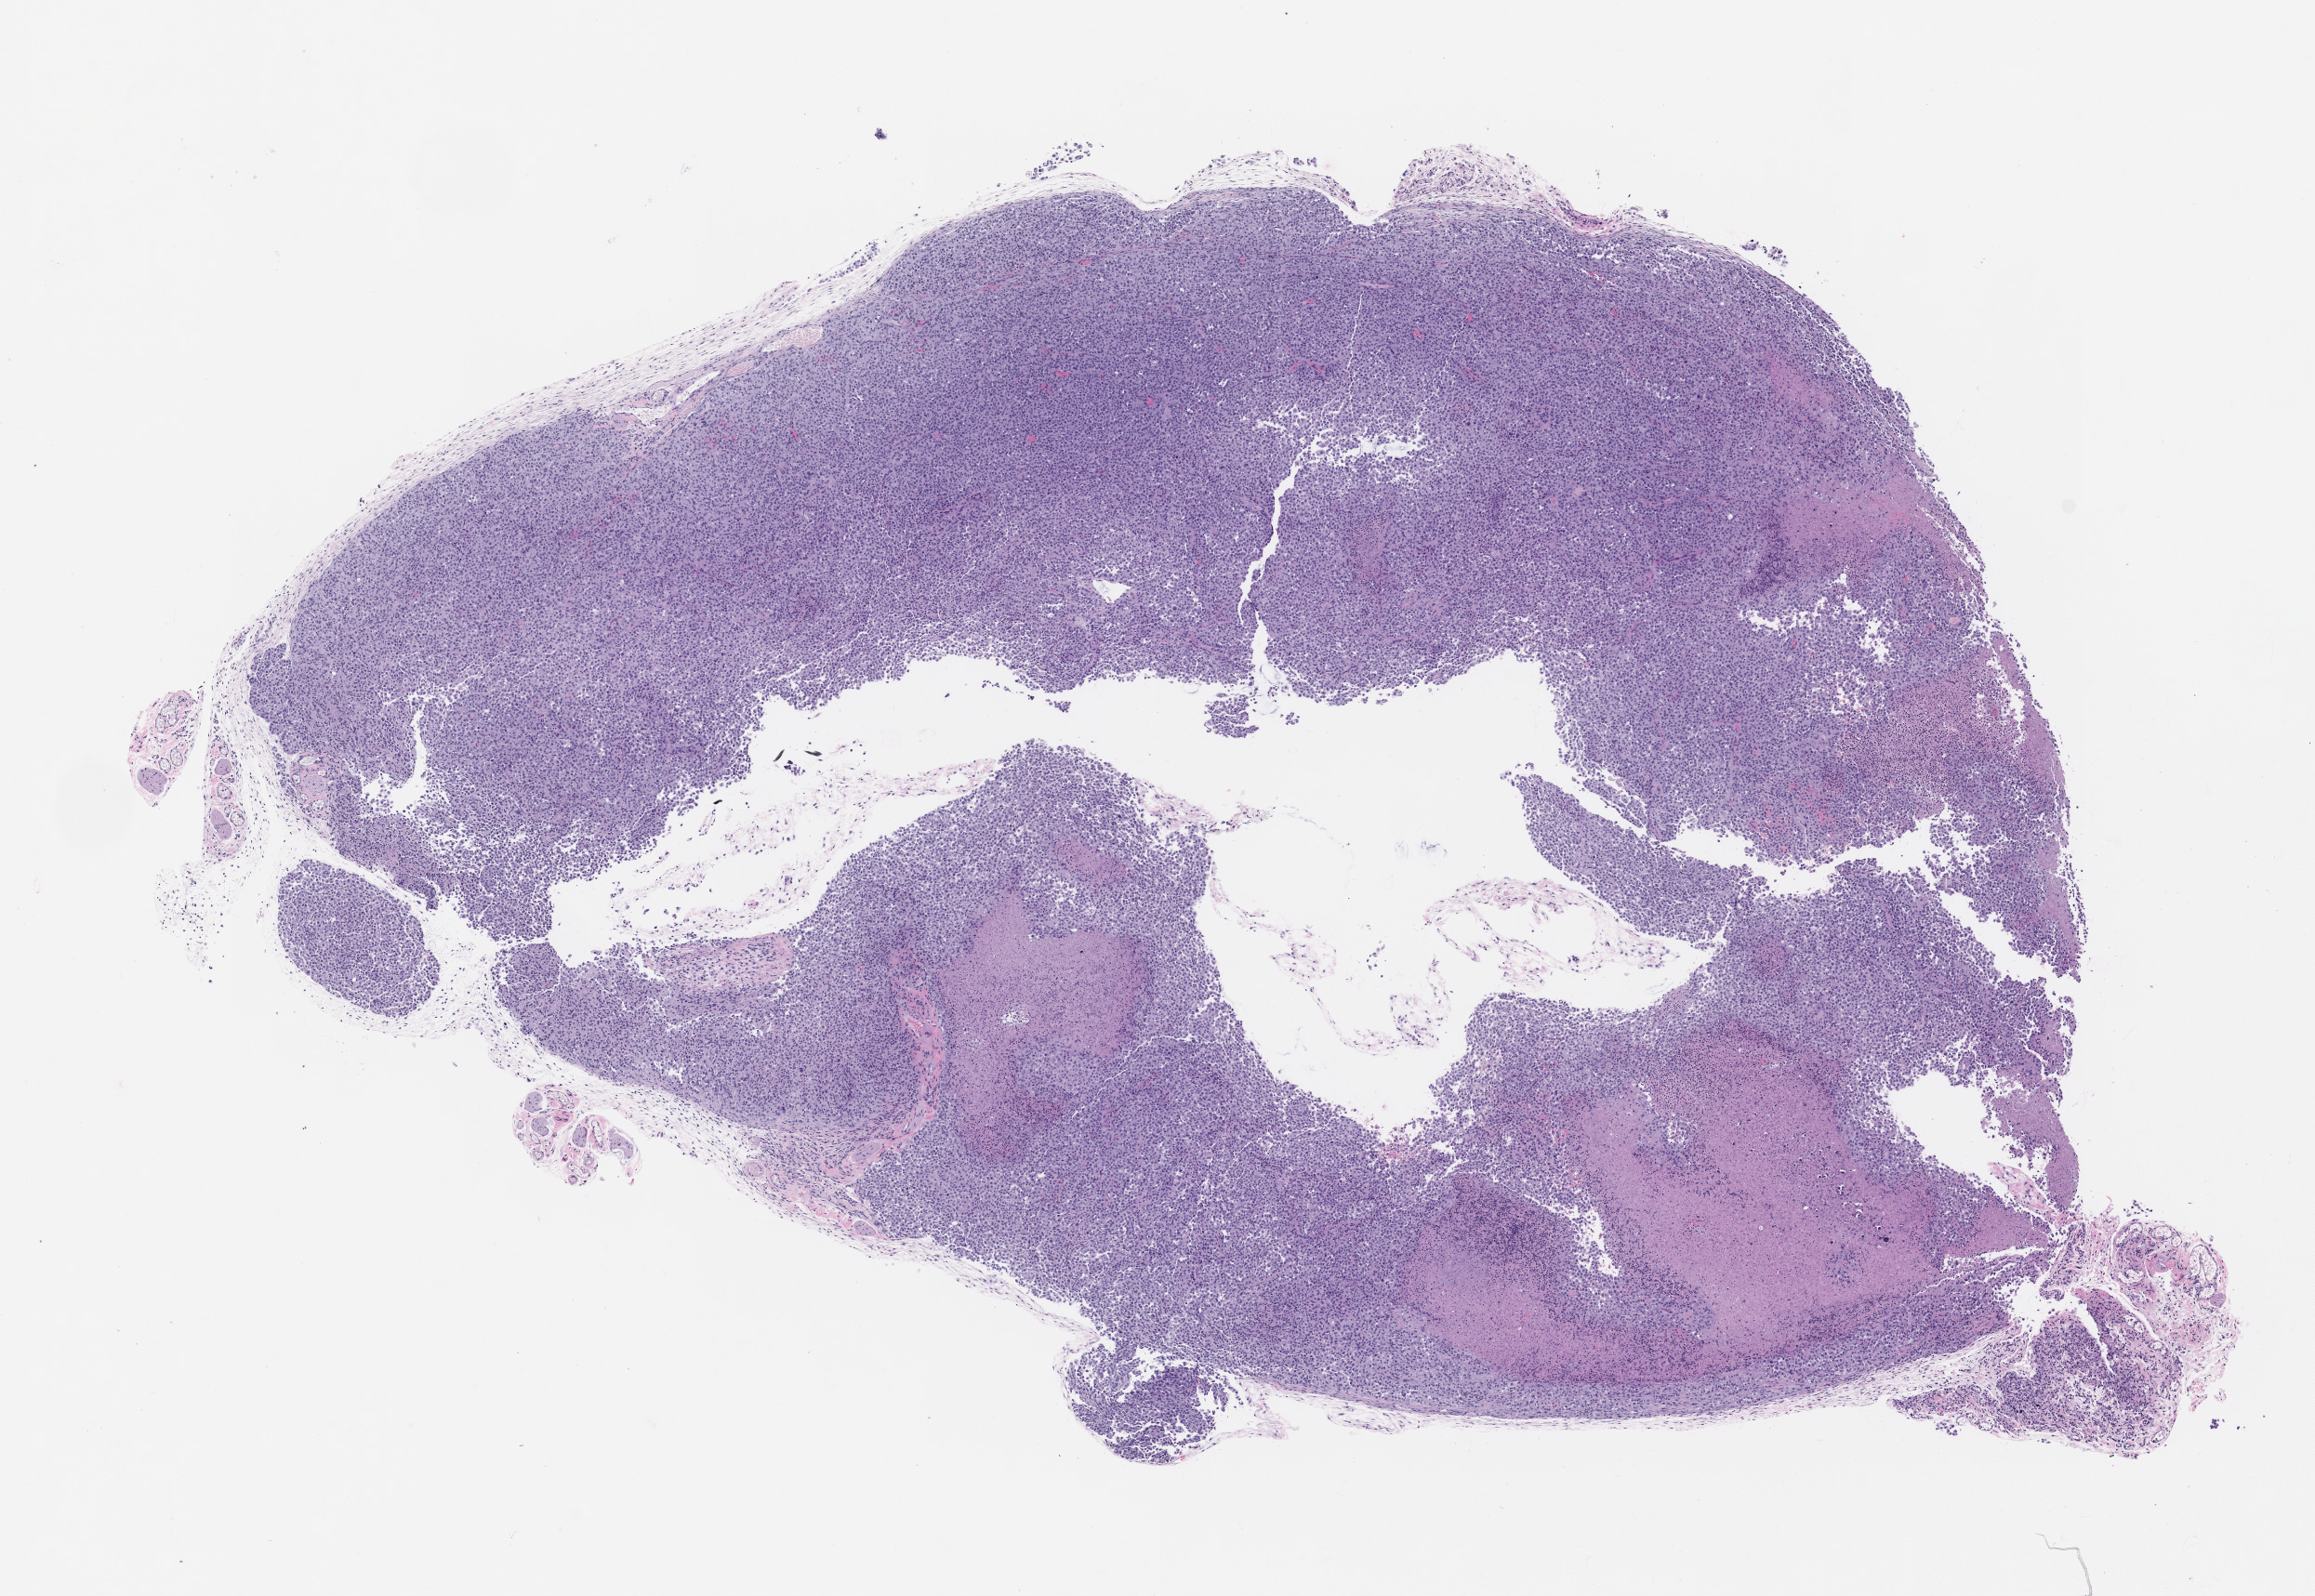
Whole-slide image, hematoxylin and eosin (H&E): patient-derived xenograft (human tumor grown in a mouse), passage 0 — whole scanned area (about 10.0 x 6.9 mm) shown as a low-resolution overview; FFPE section.
Originating patient diagnosis: Mesothelial Neoplasm.